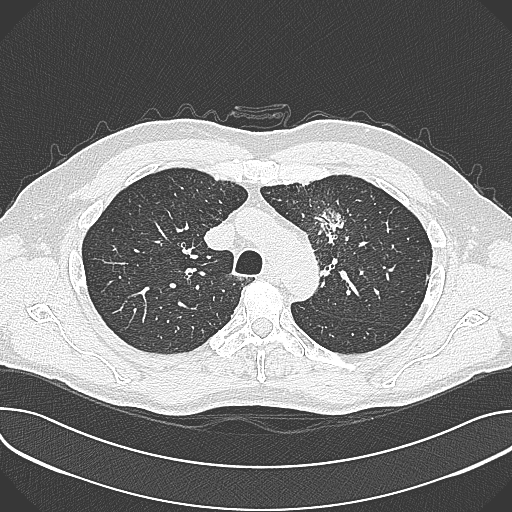
Low-dose screening chest CT, axial slice; baseline screening round; lung window (W 1500 / L -600 HU); lung (sharp) reconstruction kernel (B80f); slice 90 of 361 in the series. Male participant, aged 59 years at enrolment. Current smoker at enrolment.
Lesion marked by an expert reader, bounding box (x1, y1, x2, y2) in pixels: (301, 200, 357, 257). The screening reader recorded 2 non-calcified nodules or masses ≥4 mm on this exam (left upper lobe, left upper lobe); which of them this box marks is not recorded.